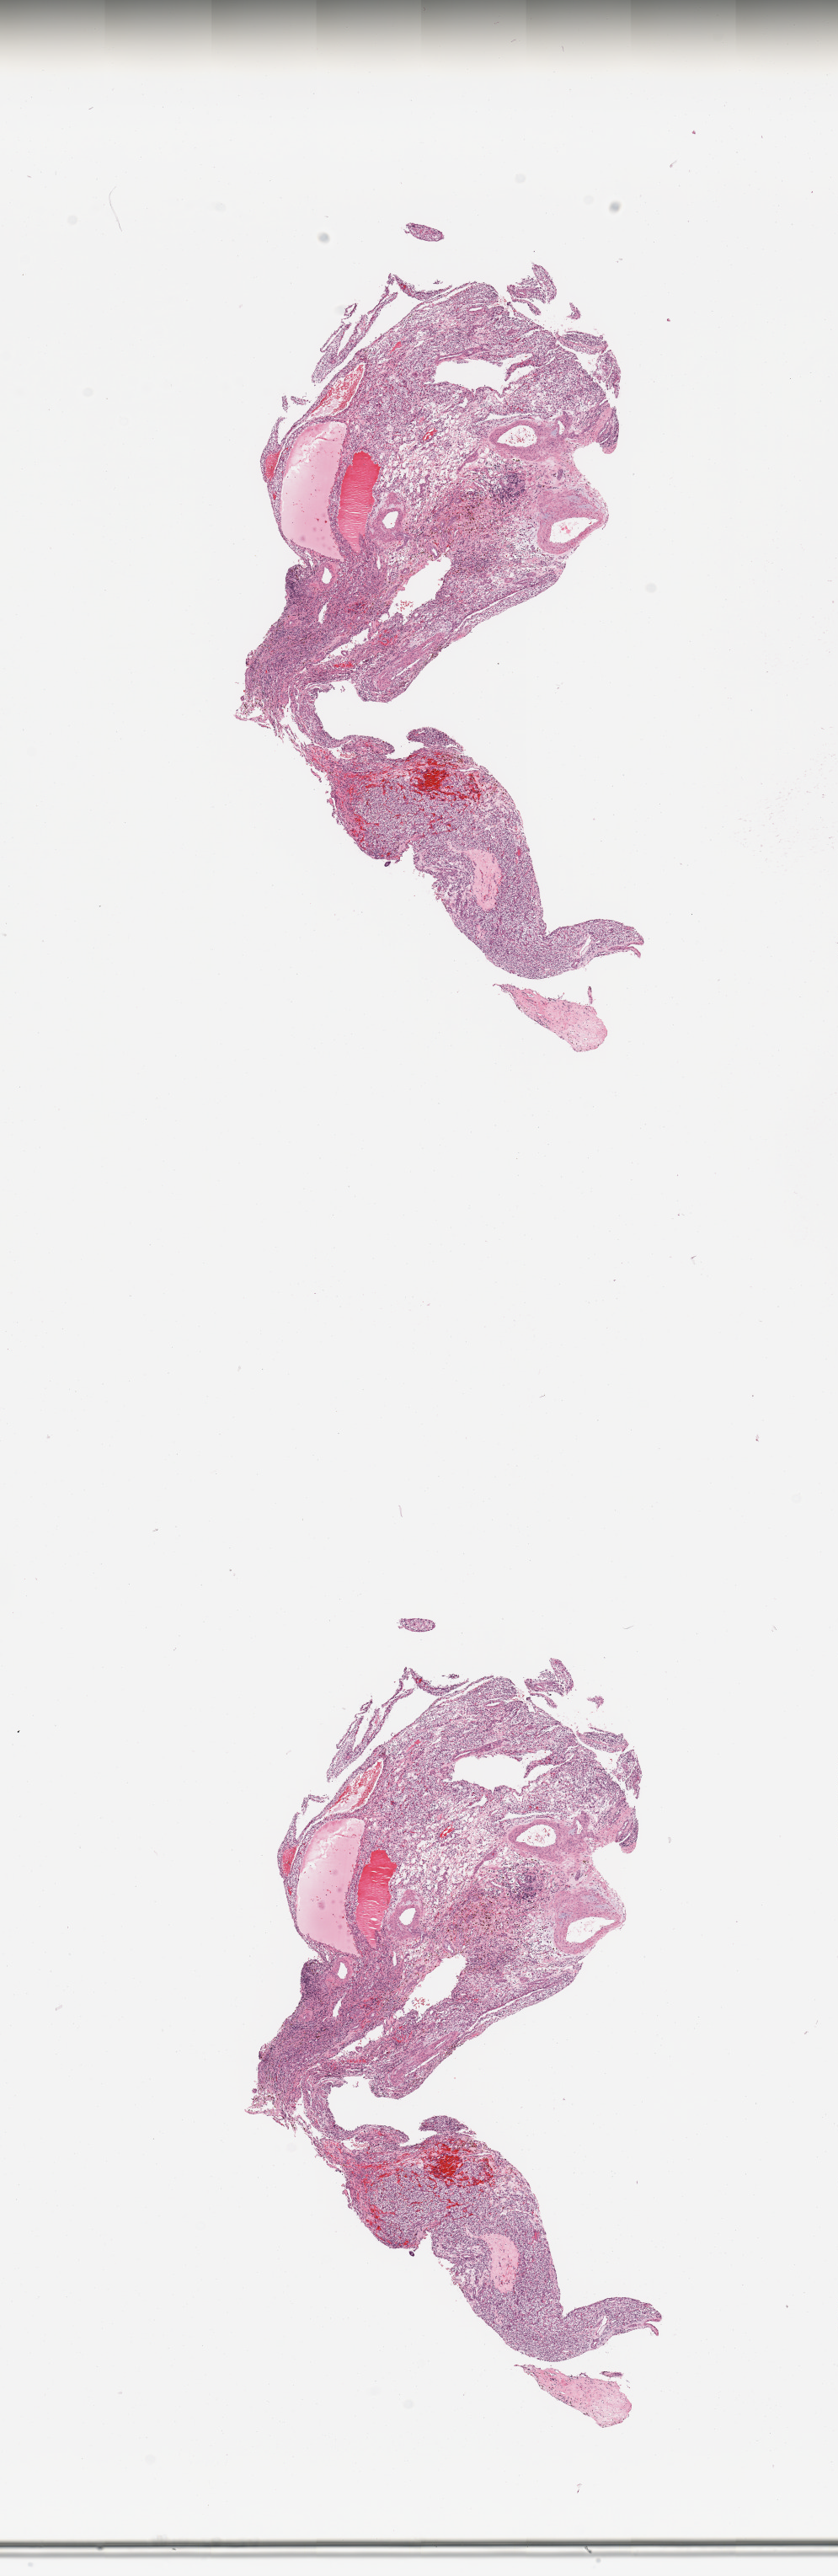
Hematoxylin and eosin (H&E) stained whole-slide image, low-resolution overview of the scanned area, about 7.9 x 24.2 mm. Kidney, tumour tissue. Male, 37 y/o. Histologic grade: G3 (poorly differentiated).
• primary tumour site (as recorded): middle
• histologic diagnosis: Renal cell carcinoma, NOS
• AJCC pathologic stage: I